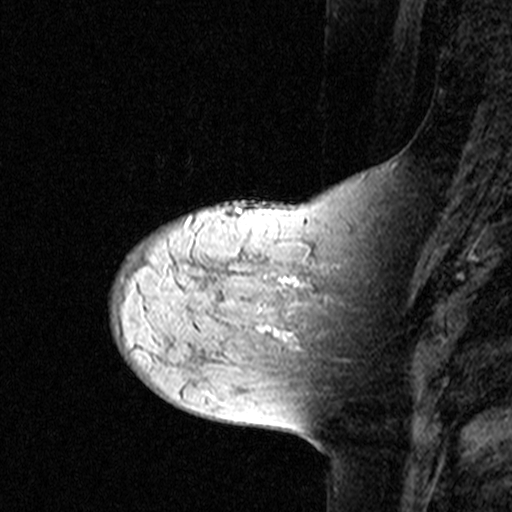
Breast MRI (dynamic contrast-enhanced), one sagittal slice. Position 11 of 44 along the scan axis. Dynamic contrast-enhanced study with each time point stored as its own series, time point 2 of 3 at this slice position (early post-contrast, ordered by acquisition time). 1.5 T. TE 4.5 ms, TR 11 ms. 3 mm slice thickness. 512 × 512 image matrix, field of view 200 × 200 mm. Patient: female, 44 years. From the clinical record (not read from this slice): setting: breast cancer imaged before/during neoadjuvant chemotherapy; receptor status: triple-negative.
Outlined on this slice (semi-automatic segmentation, software-assisted and operator-edited):
- analysis volume of interest (the breast-tissue region the enhancement analysis was run in; not a lesion): bounding box <142,208,349,363> (left, top, right, bottom; pixels)
- tumour enhancement mask (voxels above the 90 % enhancement threshold inside the analysis volume of interest): <277,281,302,340>